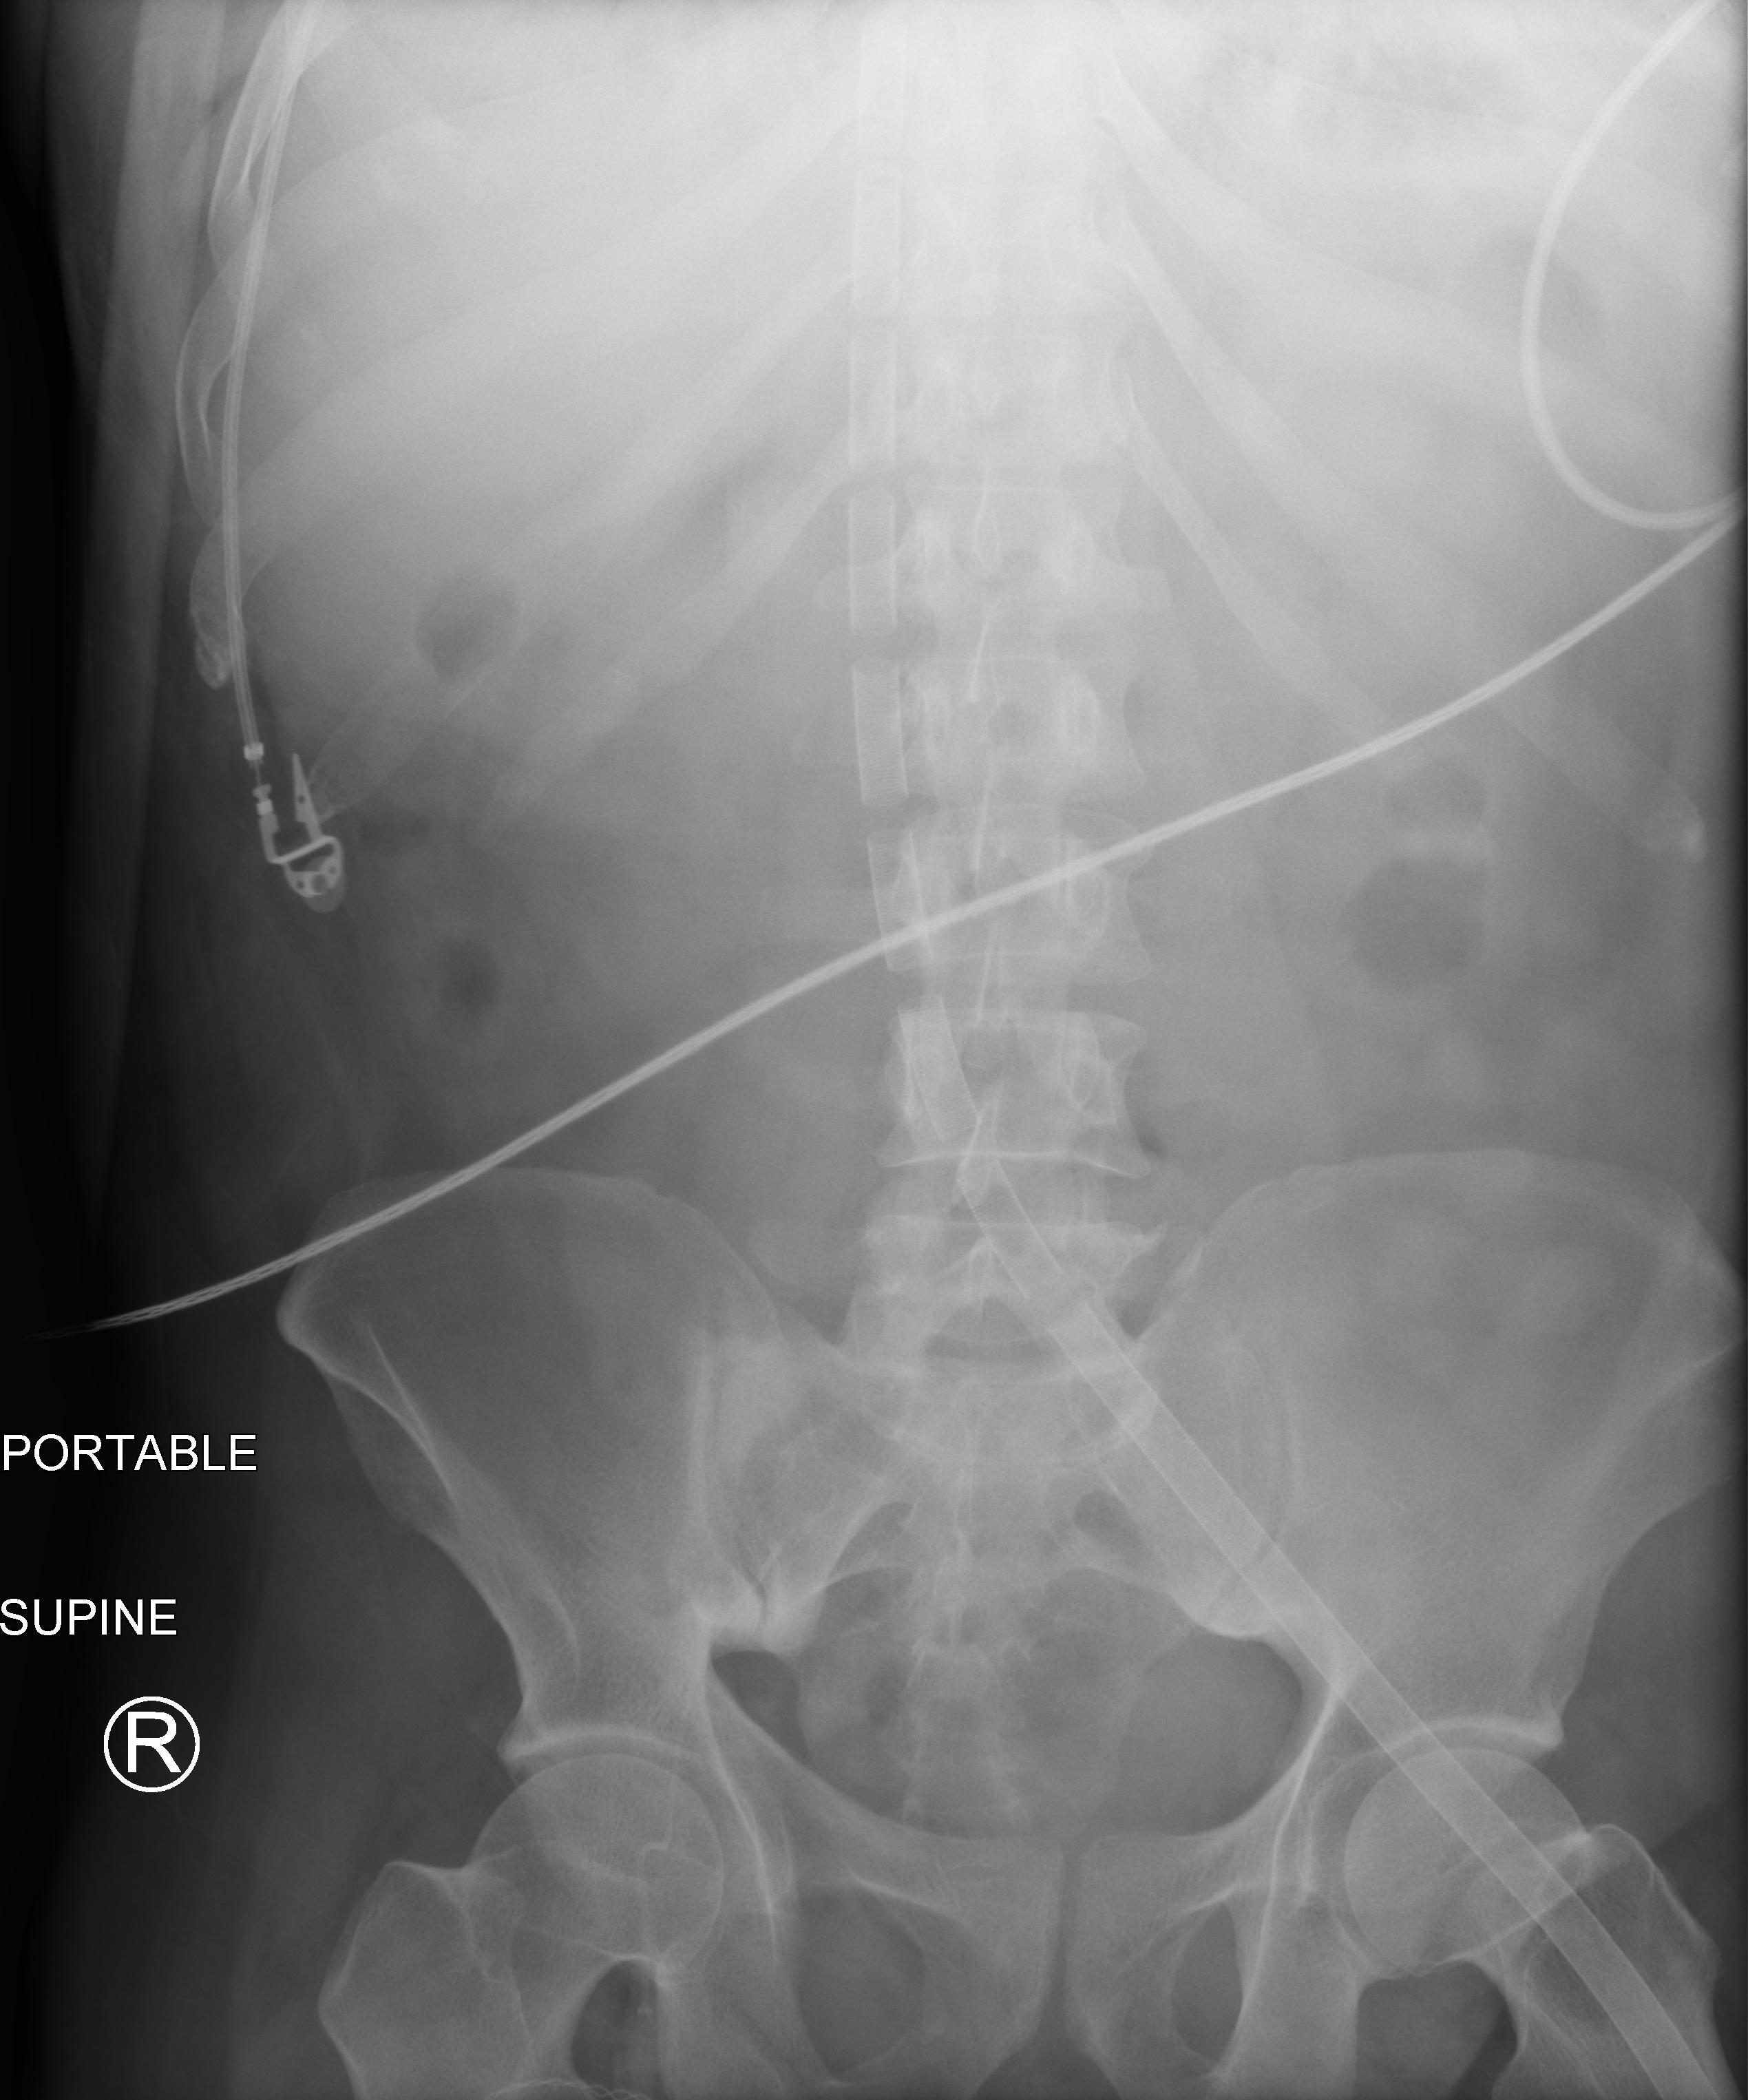
Abdomen X-ray (portable). Male patient hospitalised with COVID-19, age 18–59 years.
Admission-level facts for this patient (not findings on this image; timing relative to this image not recorded):
- mechanically ventilated during this hospital stay: yes